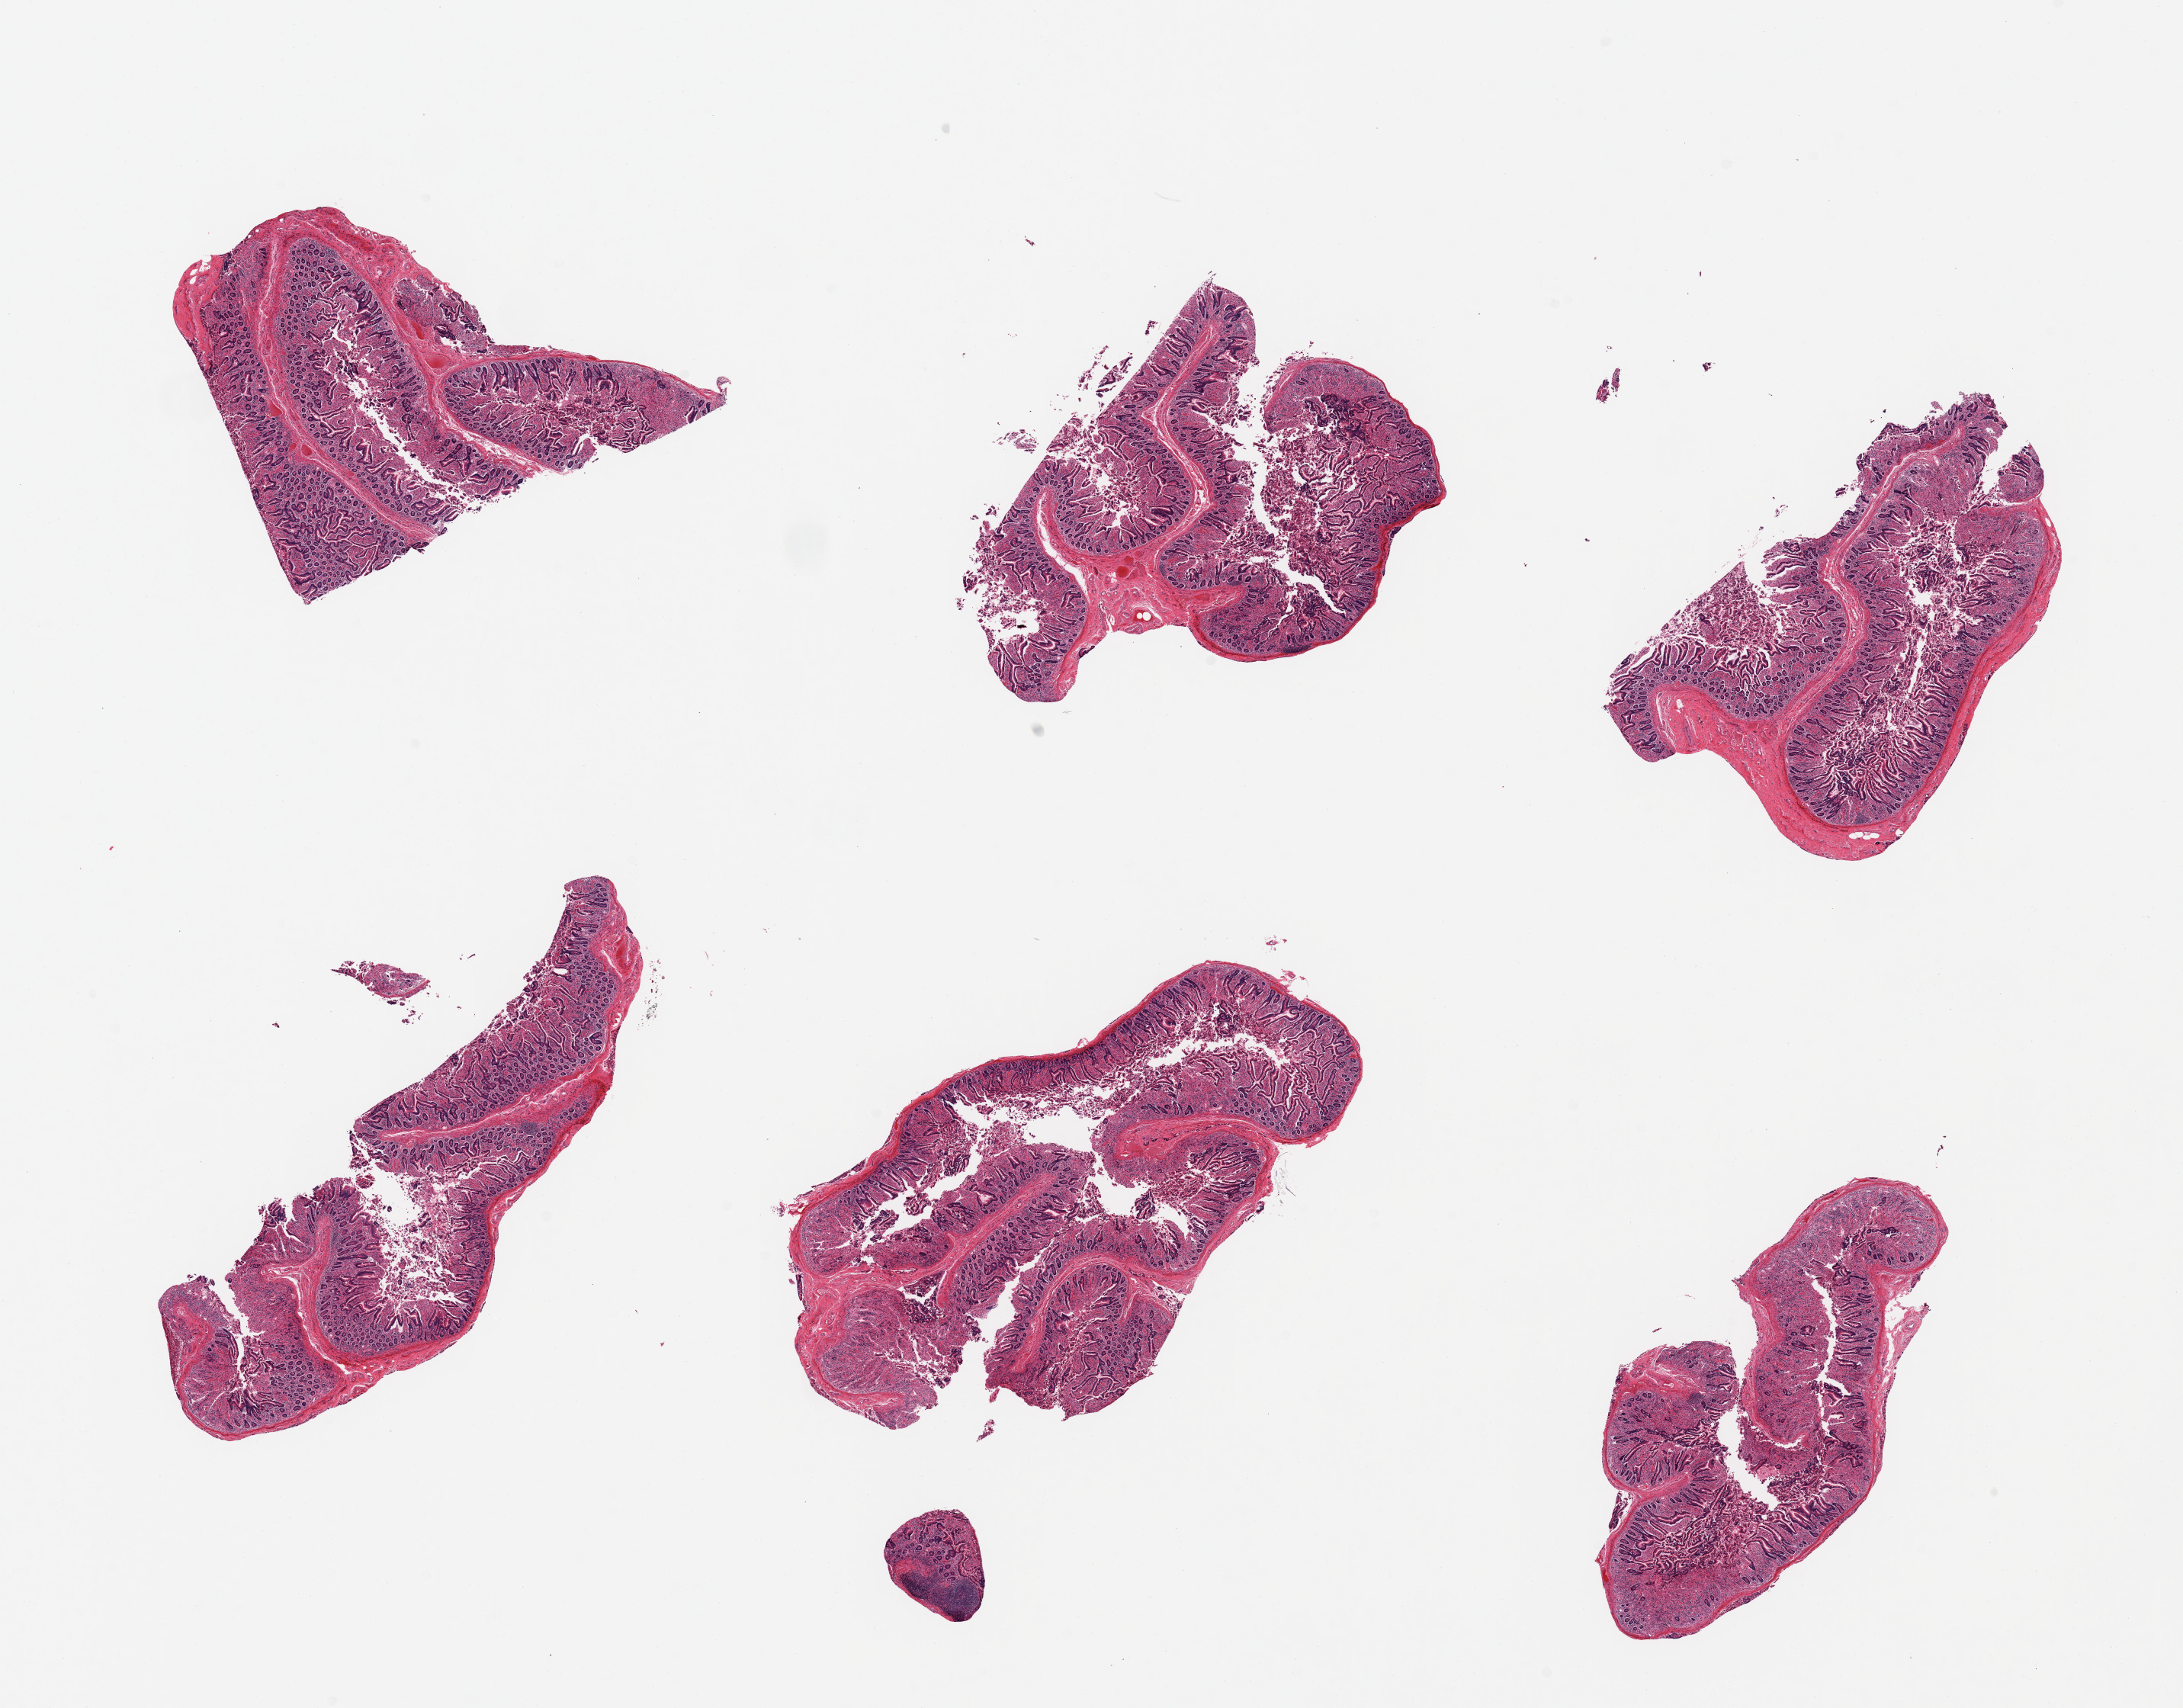
Digitized hematoxylin and eosin (H&E)-stained section — shown as a low-resolution overview of the whole scanned area (about 22.6 x 17.7 mm). Donor: female.
Specimen: PAXgene-fixed paraffin-embedded (PFPE) section; target tissue: ileum; donor tissue sample.